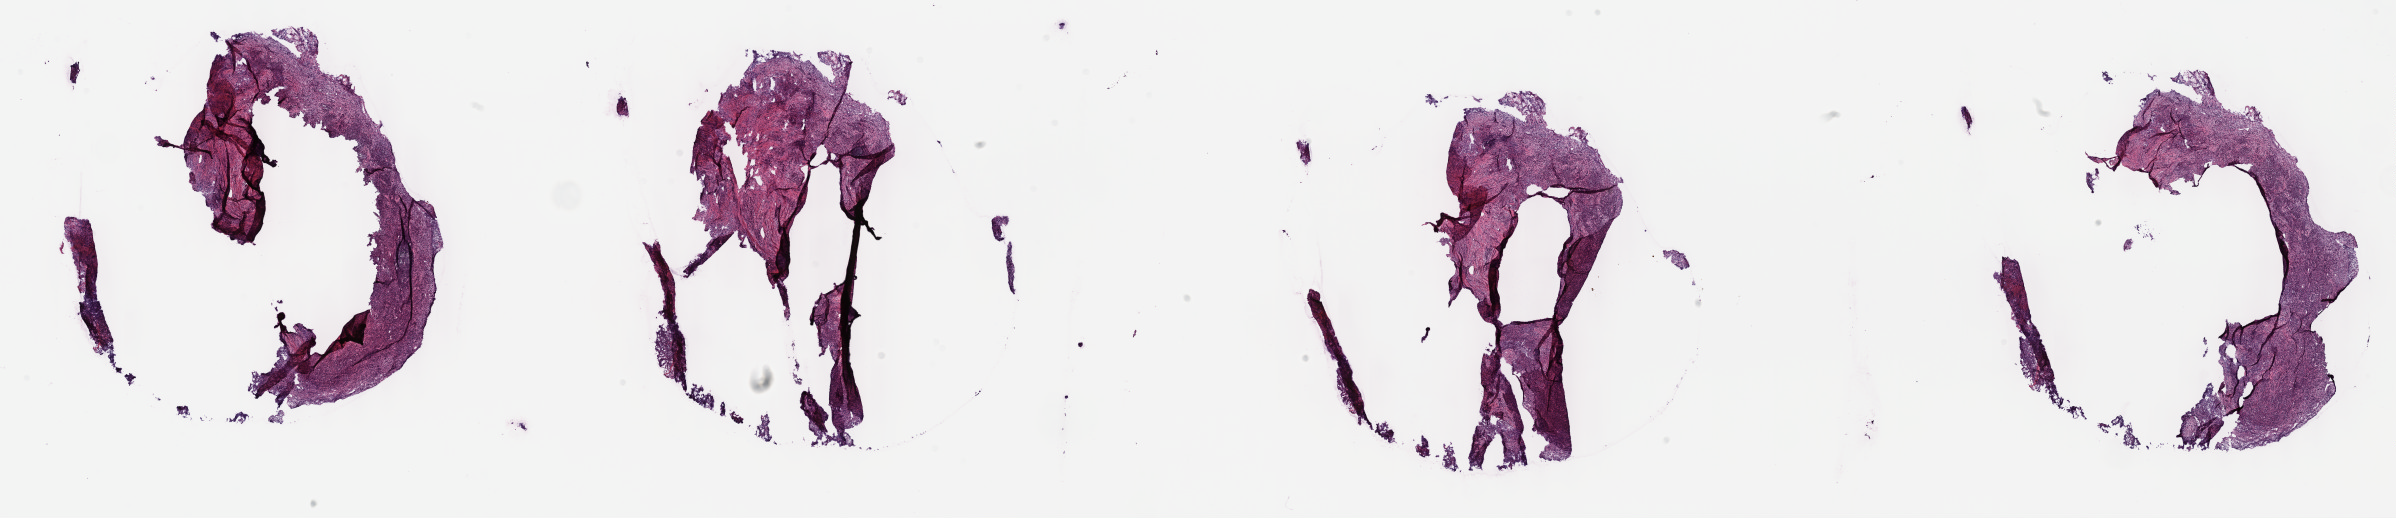
H&E whole-slide image — whole scanned area (about 38.8 x 8.4 mm, acquisition: 40x scan) shown as a low-resolution overview. Frozen section from the top of the tissue portion. Primary tumour sample from the mesothelium. Female, age 65 years at initial diagnosis. Slide review estimates, as recorded: tumour cells 100%, tumour nuclei 80%.
Pathologic diagnosis: Mesothelioma, biphasic, malignant (pleura, NOS).